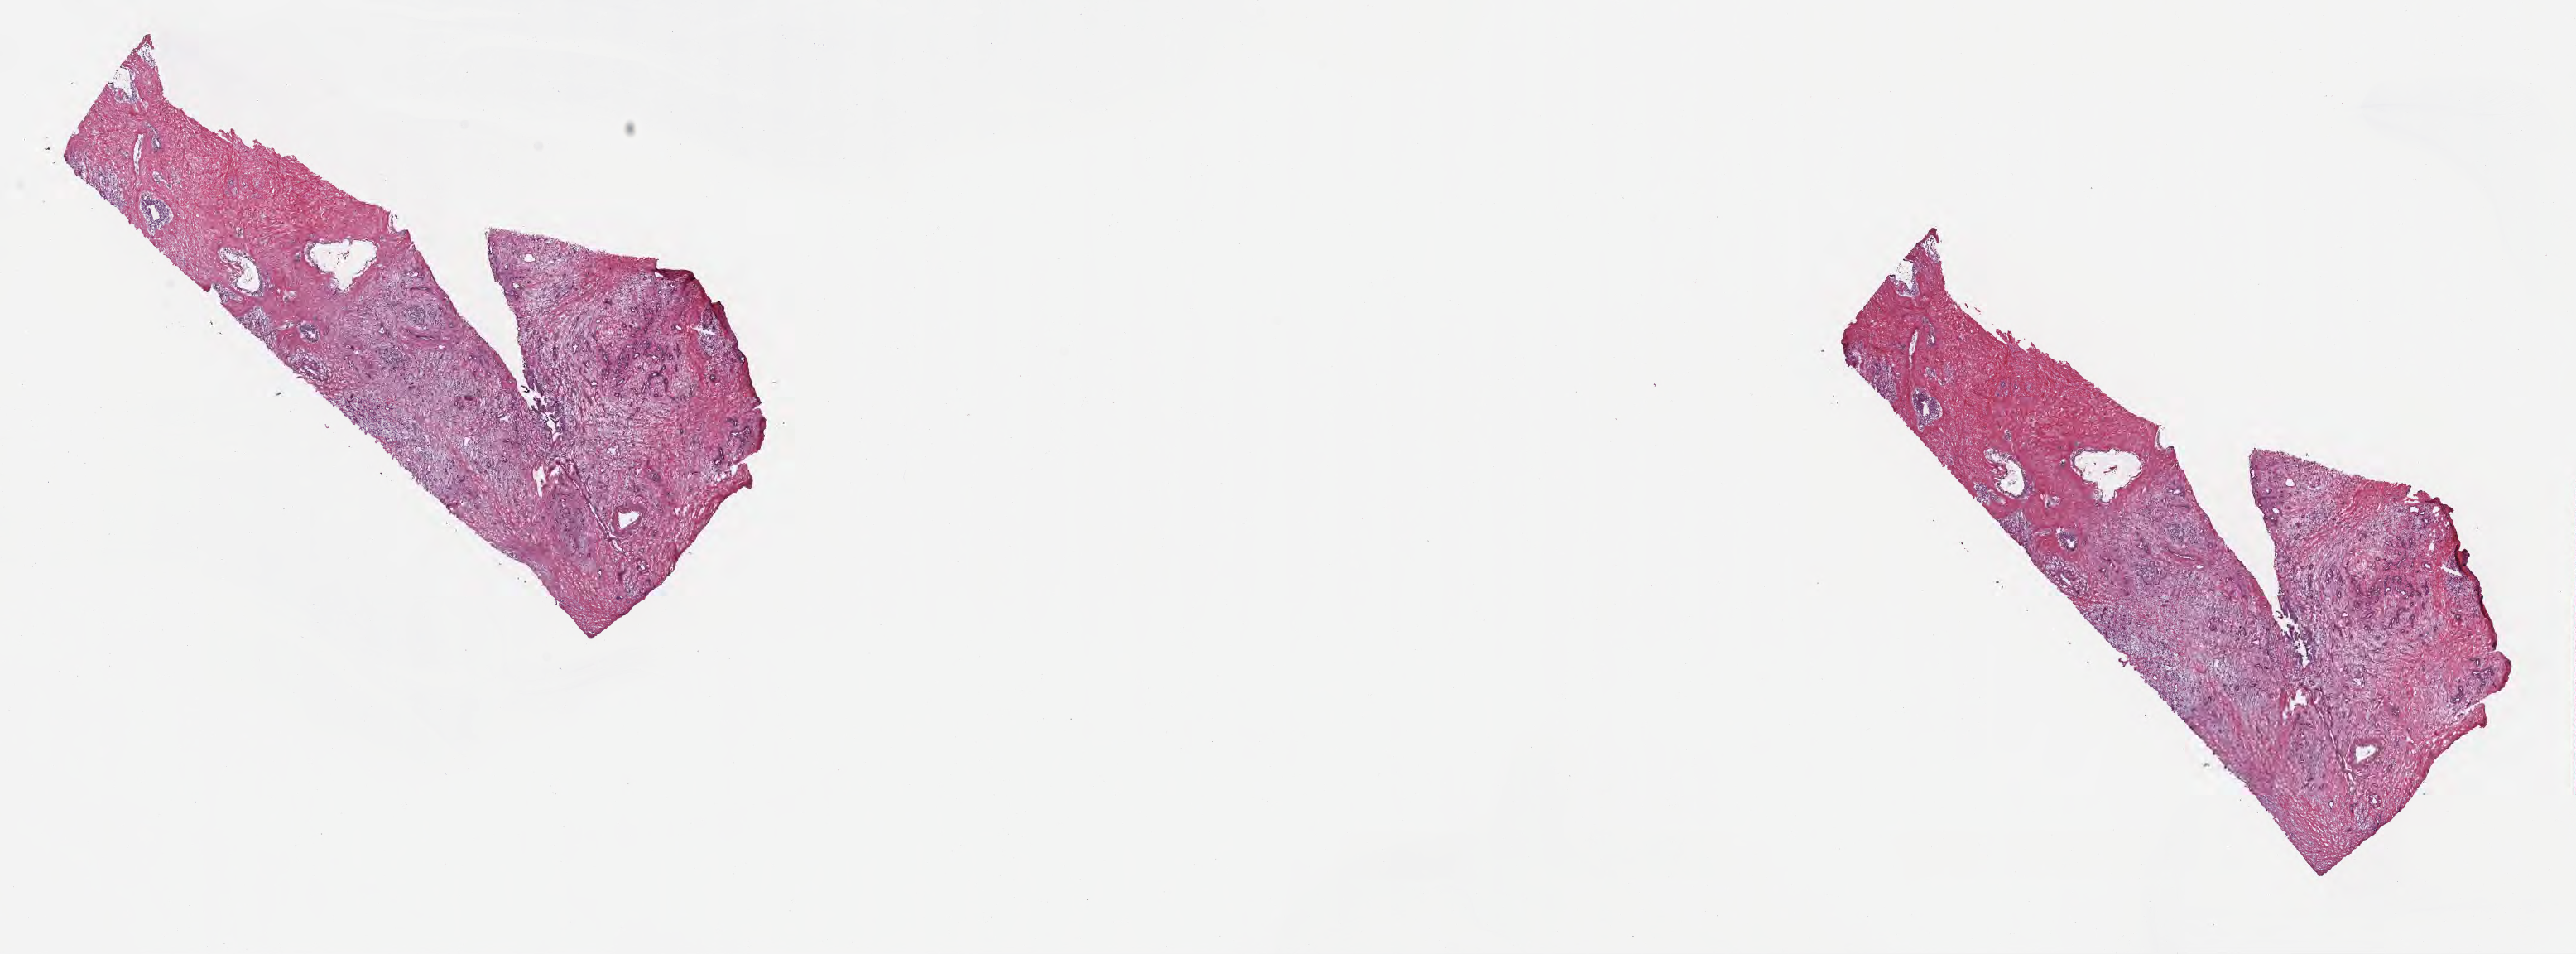
Whole-slide image, haematoxylin and eosin stain, shown as a low-resolution overview of the whole scanned area (about 25.2 x 9.3 mm); frozen section; specimen: primary tumor; site: head of pancreas. Patient: female, age at initial diagnosis 70 years. Tumor grade: G2 (moderately differentiated). Composition of this section per pathologist review: tumor cells 40%, tumor nuclei 50%, stromal cells 60%, necrosis 0%, normal cells 0%. Inflammatory infiltration, as recorded: lymphocyte infiltration 0%, monocyte infiltration 0%, neutrophil infiltration 0%.
* histologic diagnosis: Infiltrating duct carcinoma, NOS
* AJCC pathologic stage: Stage IIB